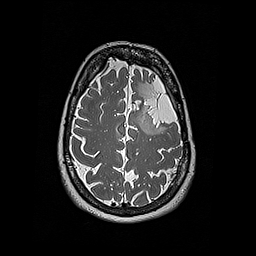
Brain MRI from a brain-tumour surgery series, one axial slice. Slice 137 of 192 in the series (ordered by position). 1 mm slice thickness. 256 × 256 image matrix, field of view 250 × 250 mm. Case-level facts recorded for this patient, not image findings: histopathology: Oligodendroglioma; WHO grade: 2; IDH mutation: yes; tumour location: Left Frontal.
Outlined on this slice (outlined manually by an expert reader):
- tumour: bounding box [x1, y1, x2, y2] px = [143, 115, 157, 134]